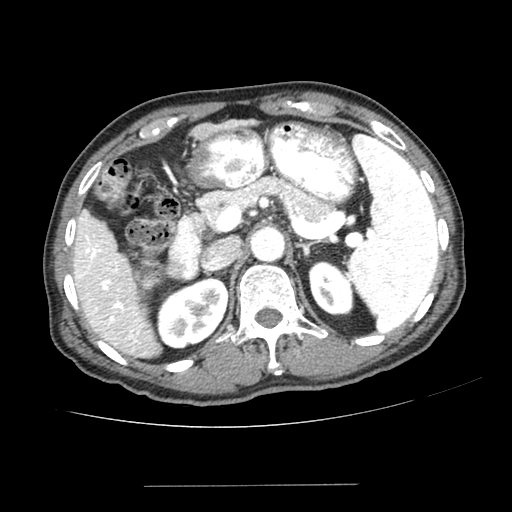
Contrast-enhanced abdominal CT (liver protocol), one axial slice. Position 147 of 187 along the scan axis. 100 kVp. One of 2 acquisitions stored at this slice position. Soft-tissue window (W 400 / L 40 HU). 512 × 512 image matrix, field of view 360 × 360 mm. From the clinical record (not read from this slice): diagnosis: hepatocellular carcinoma (patient treated with transarterial chemoembolisation; whether this scan precedes or follows treatment is not stated here); TNM stage (as recorded): Stage-I; Child-Pugh class: A; tumour differentiation: poorly differentiated; tumour nodularity: uninodular.
Annotated regions visible in this slice (semi-automatic segmentation, software-assisted and operator-edited):
- liver parenchyma outside the tumour (the mass and vessels are separate outlines, so this box may not span the whole liver): bounding box [x1, y1, x2, y2] px = [72, 210, 160, 356]
- liver vessels: [77, 219, 139, 343]